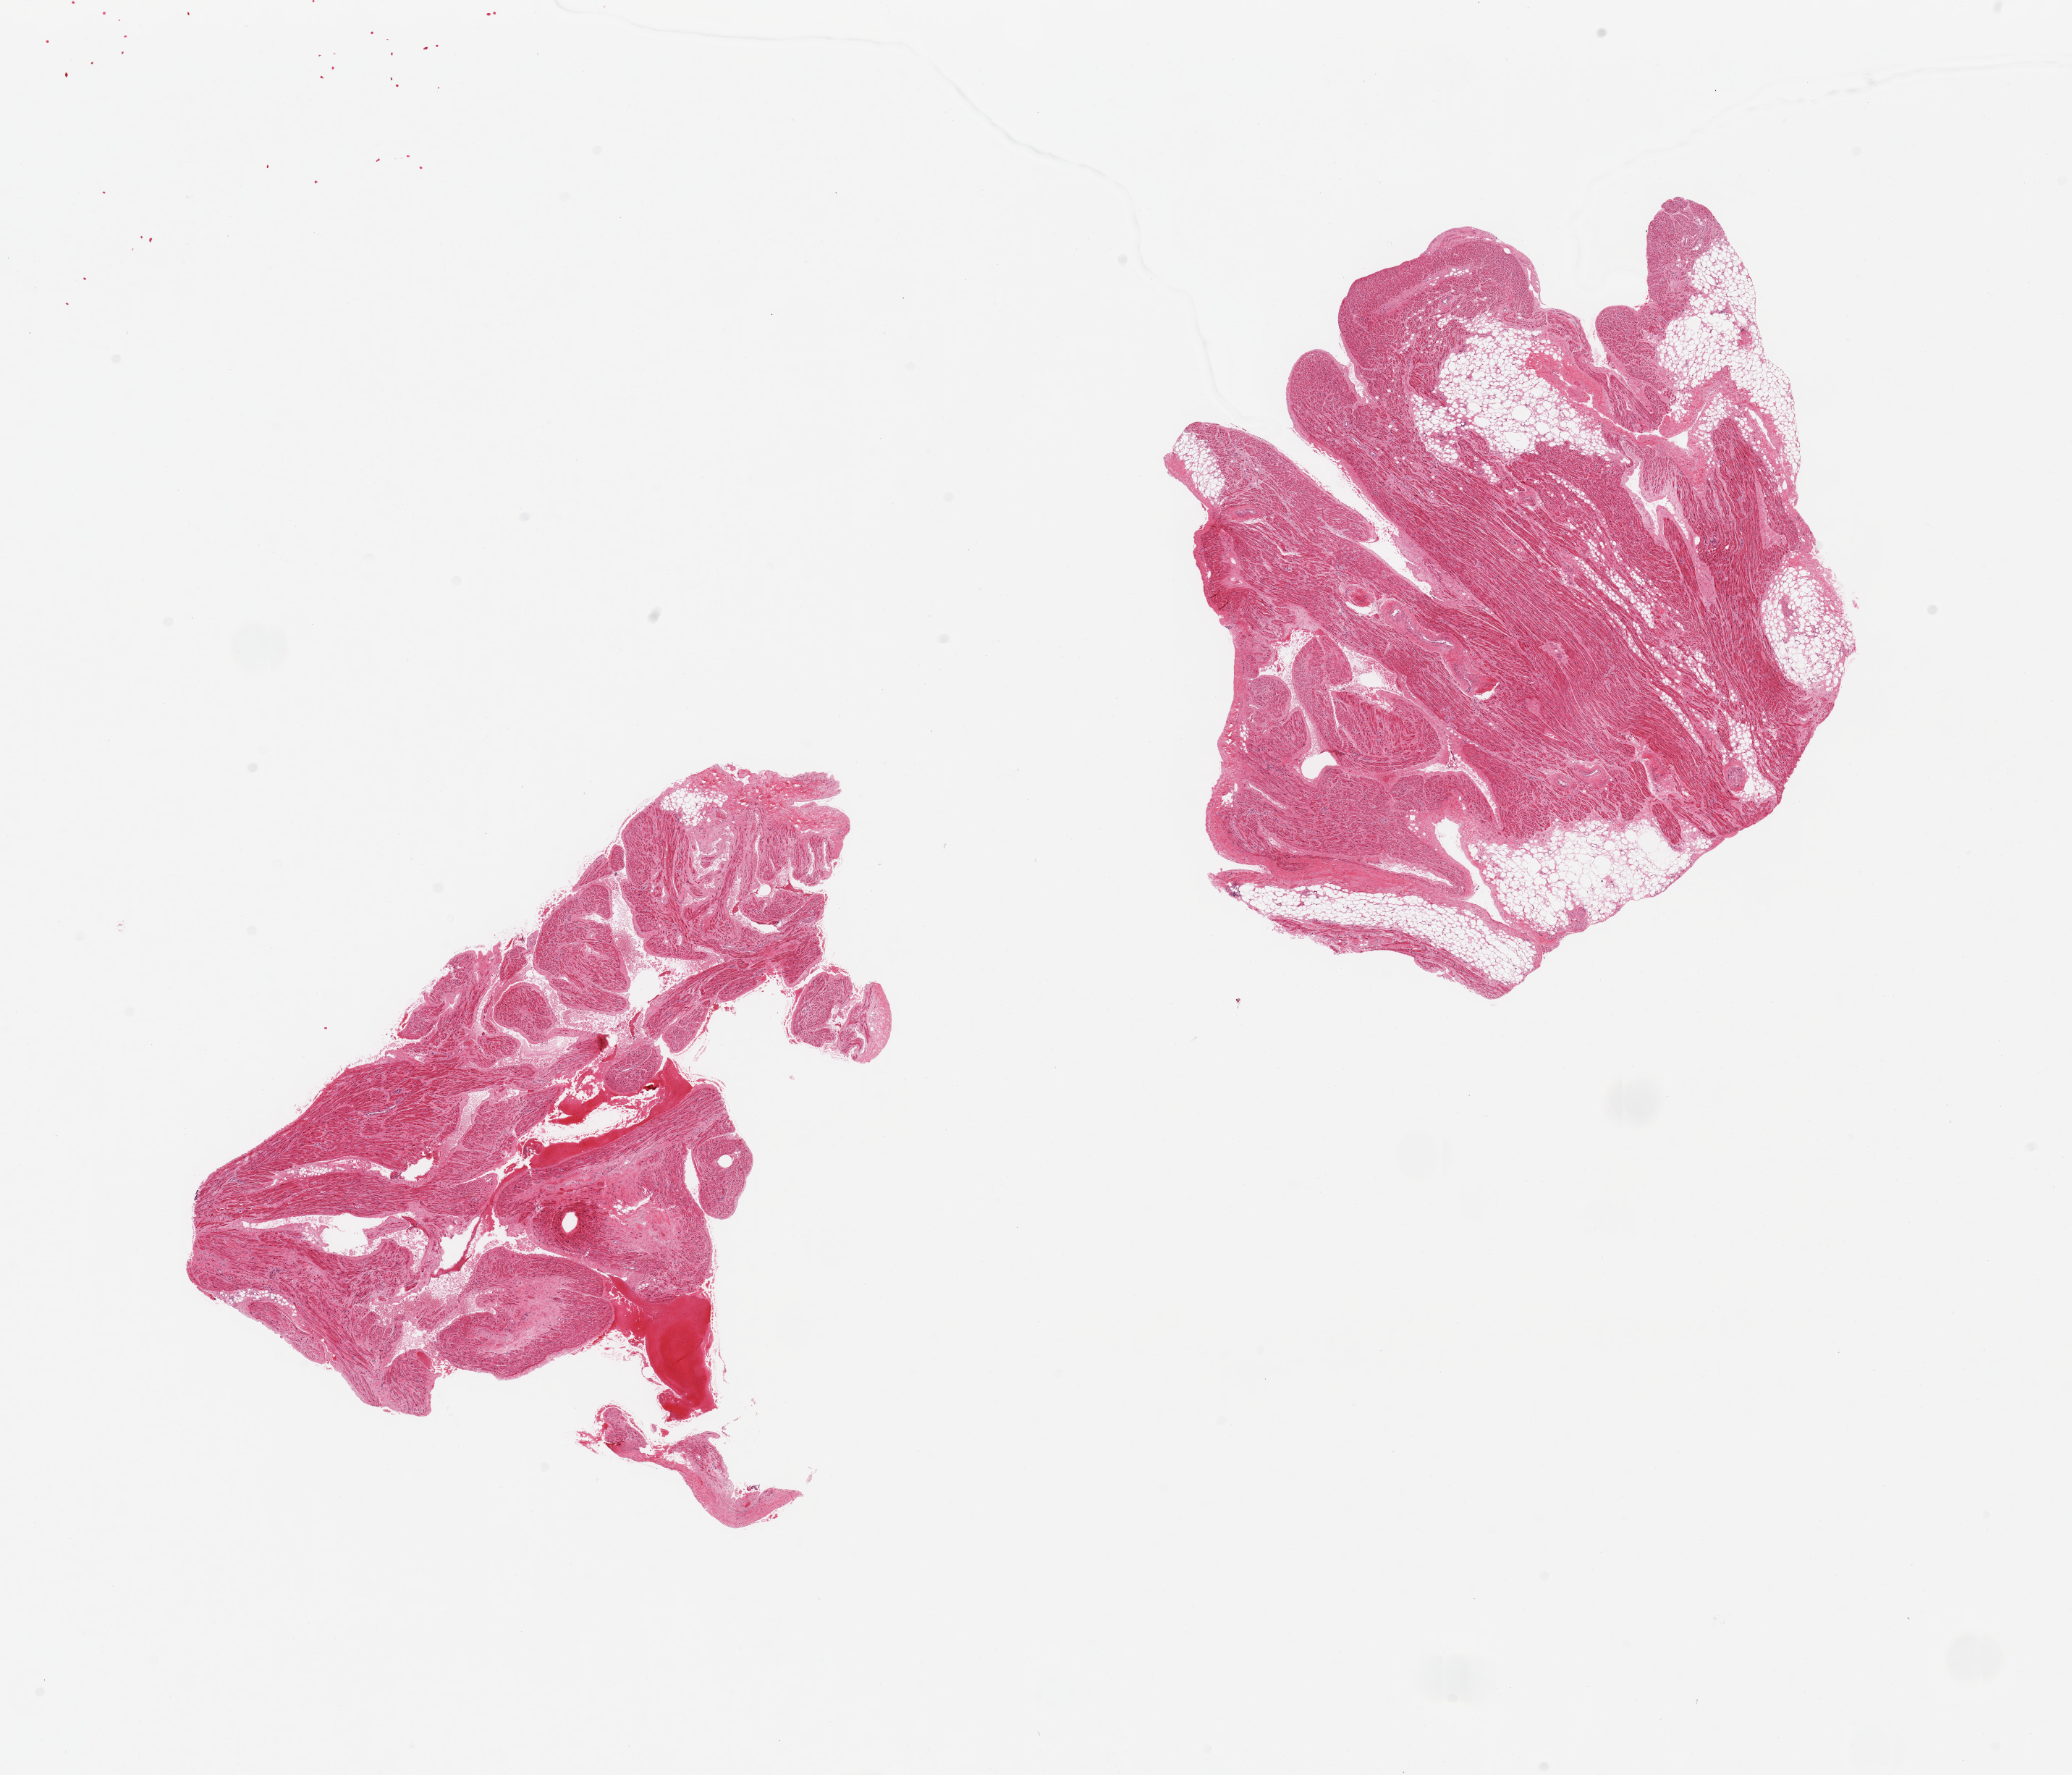
Digitized haematoxylin and eosin-stained section — a low-resolution overview of the entire scanned area, about 22.6 x 19.4 mm (acquisition: 20x scan), PAXgene-fixed paraffin-embedded (PFPE) section, sampled site (target tissue): auricular appendage, donor tissue sample. Donor: male.
Review note (as recorded): 2 pieces; one piece is ~25% fat.